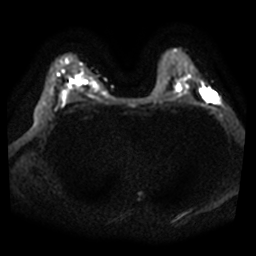
Breast MRI, one axial slice. Slice 28 of 38 in the series (ordered by position). Diffusion-weighted series; image 2 of 4 stored at this slice position (different b-values; order by instance number). 3 T. 5 mm slice thickness. 256 × 256 image matrix, field of view 360 × 360 mm. Female patient.
Annotated regions visible in this slice (expert manual segmentation):
- tumour on diffusion-weighted imaging: bounding box [x1, y1, x2, y2] px = [204, 91, 218, 103]